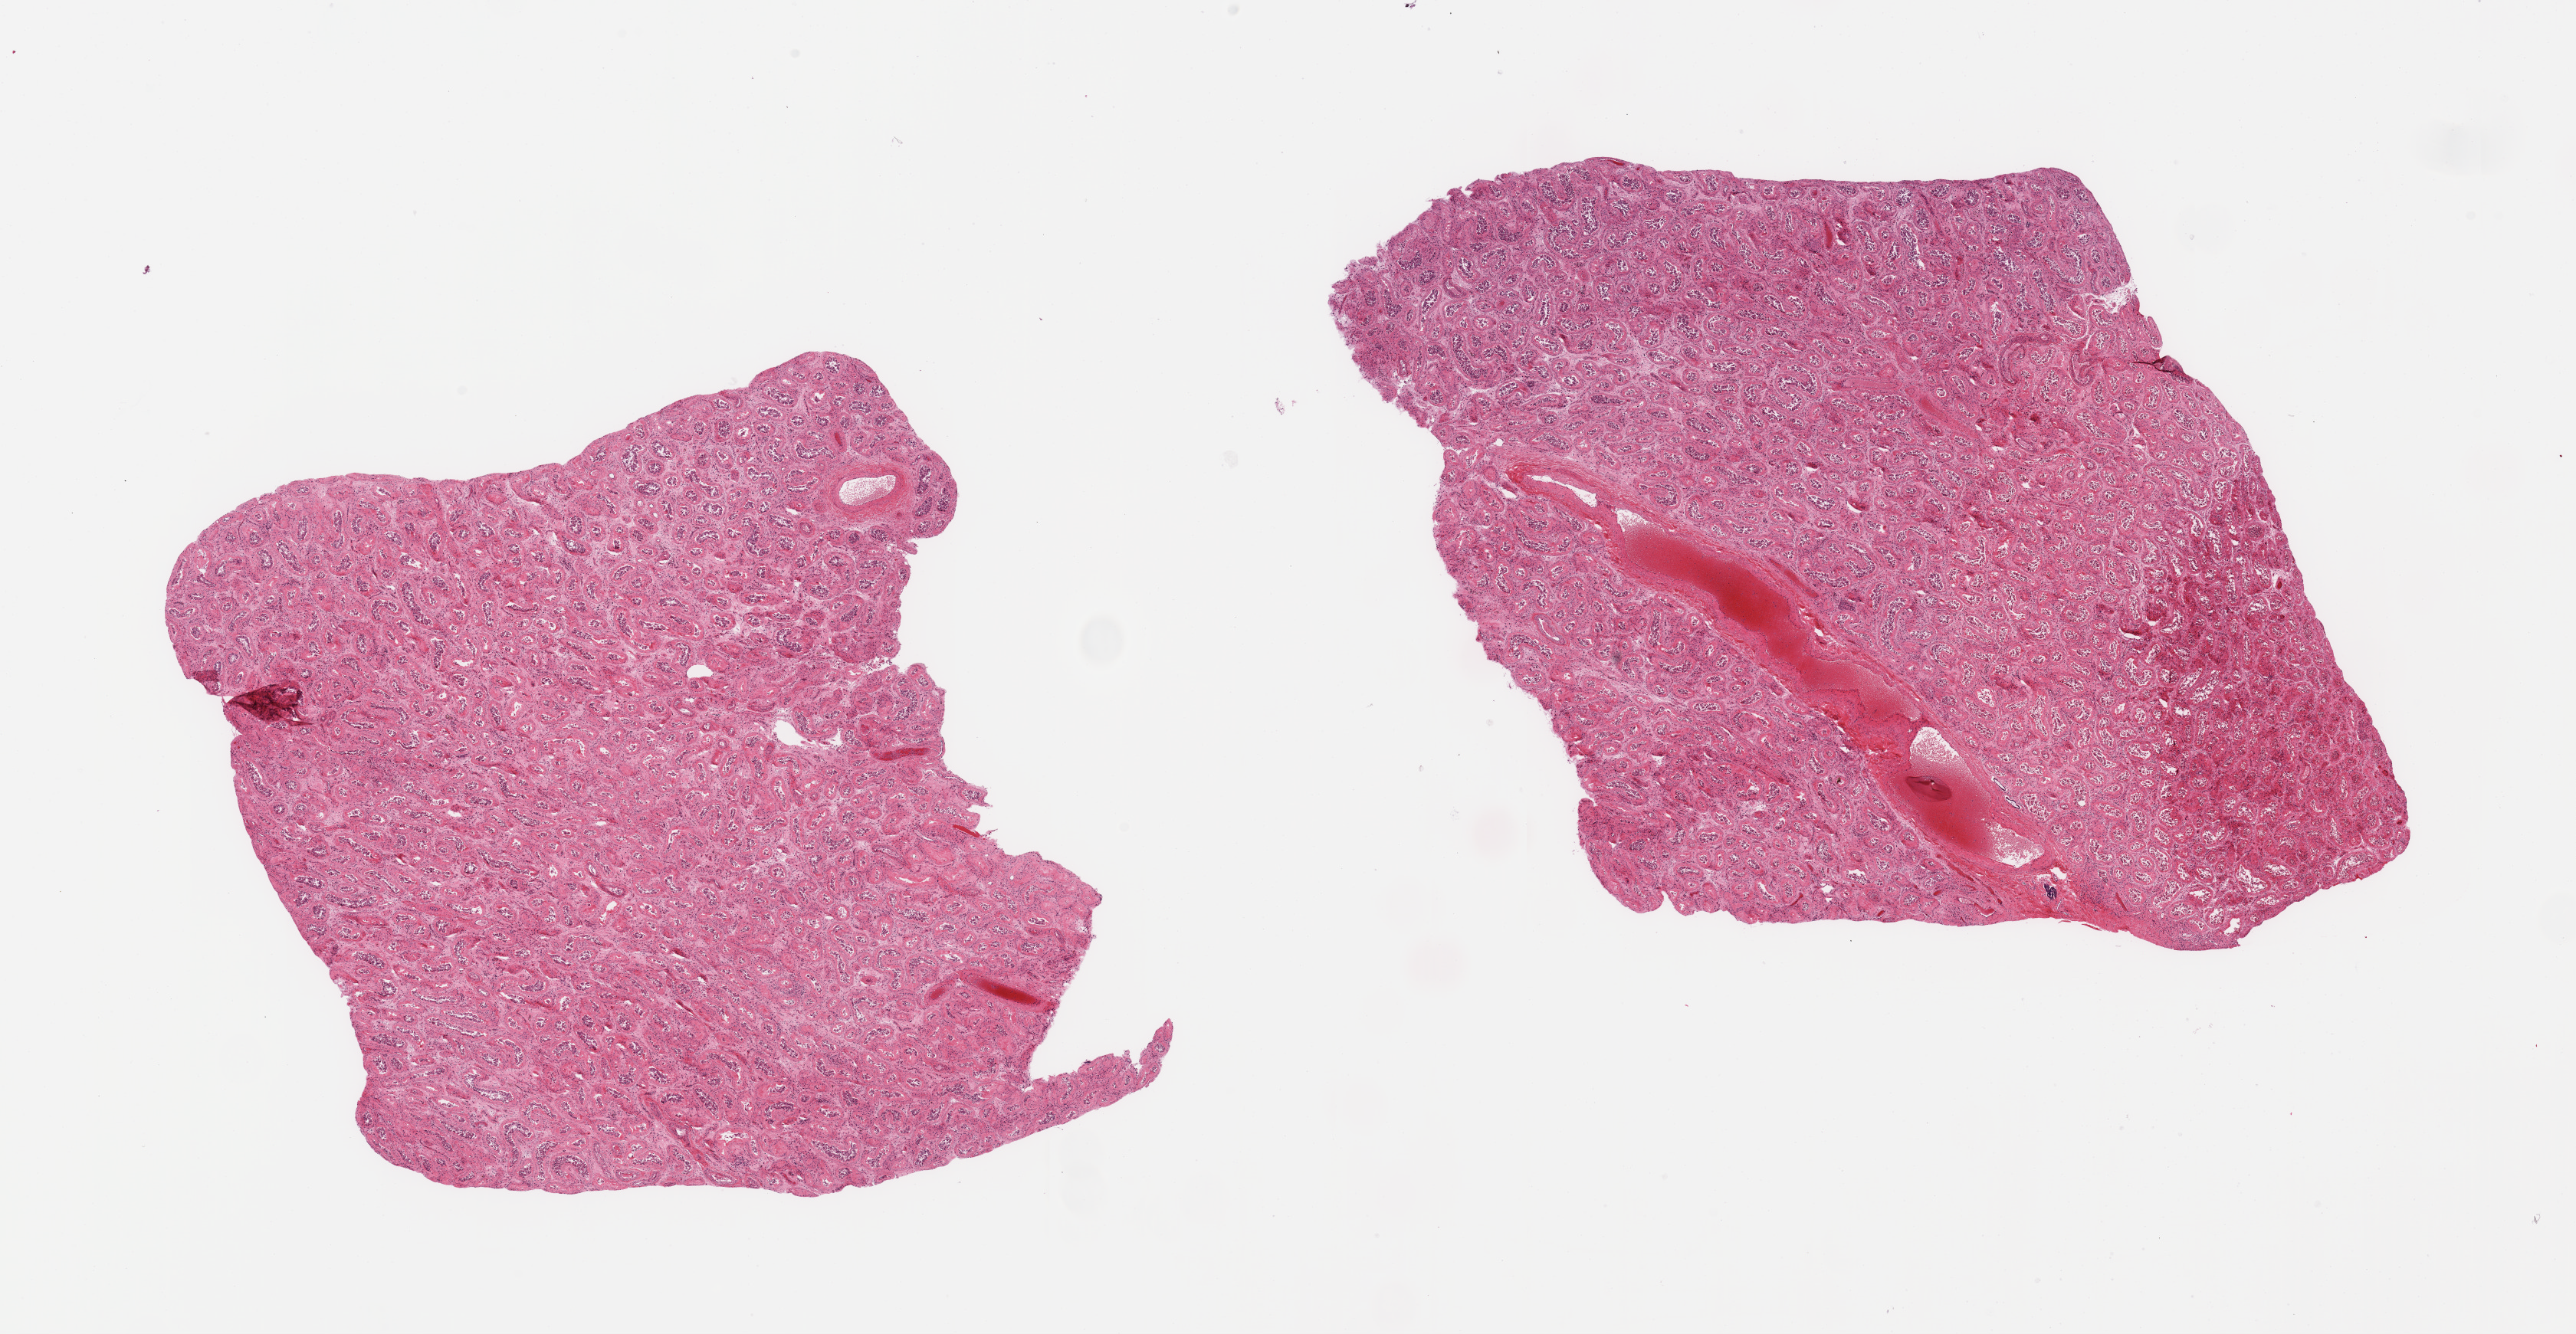
Digitized H&E-stained section — whole scanned area (about 26.6 x 13.8 mm, acquisition: 20x scan) shown as a low-resolution overview. PAXgene-fixed, paraffin-embedded tissue. Sampled site (target tissue): testis. Donor tissue sample.
Reviewer comment on this tissue sample: 2 pieces; moderately sclerosed with tubular atrophy.